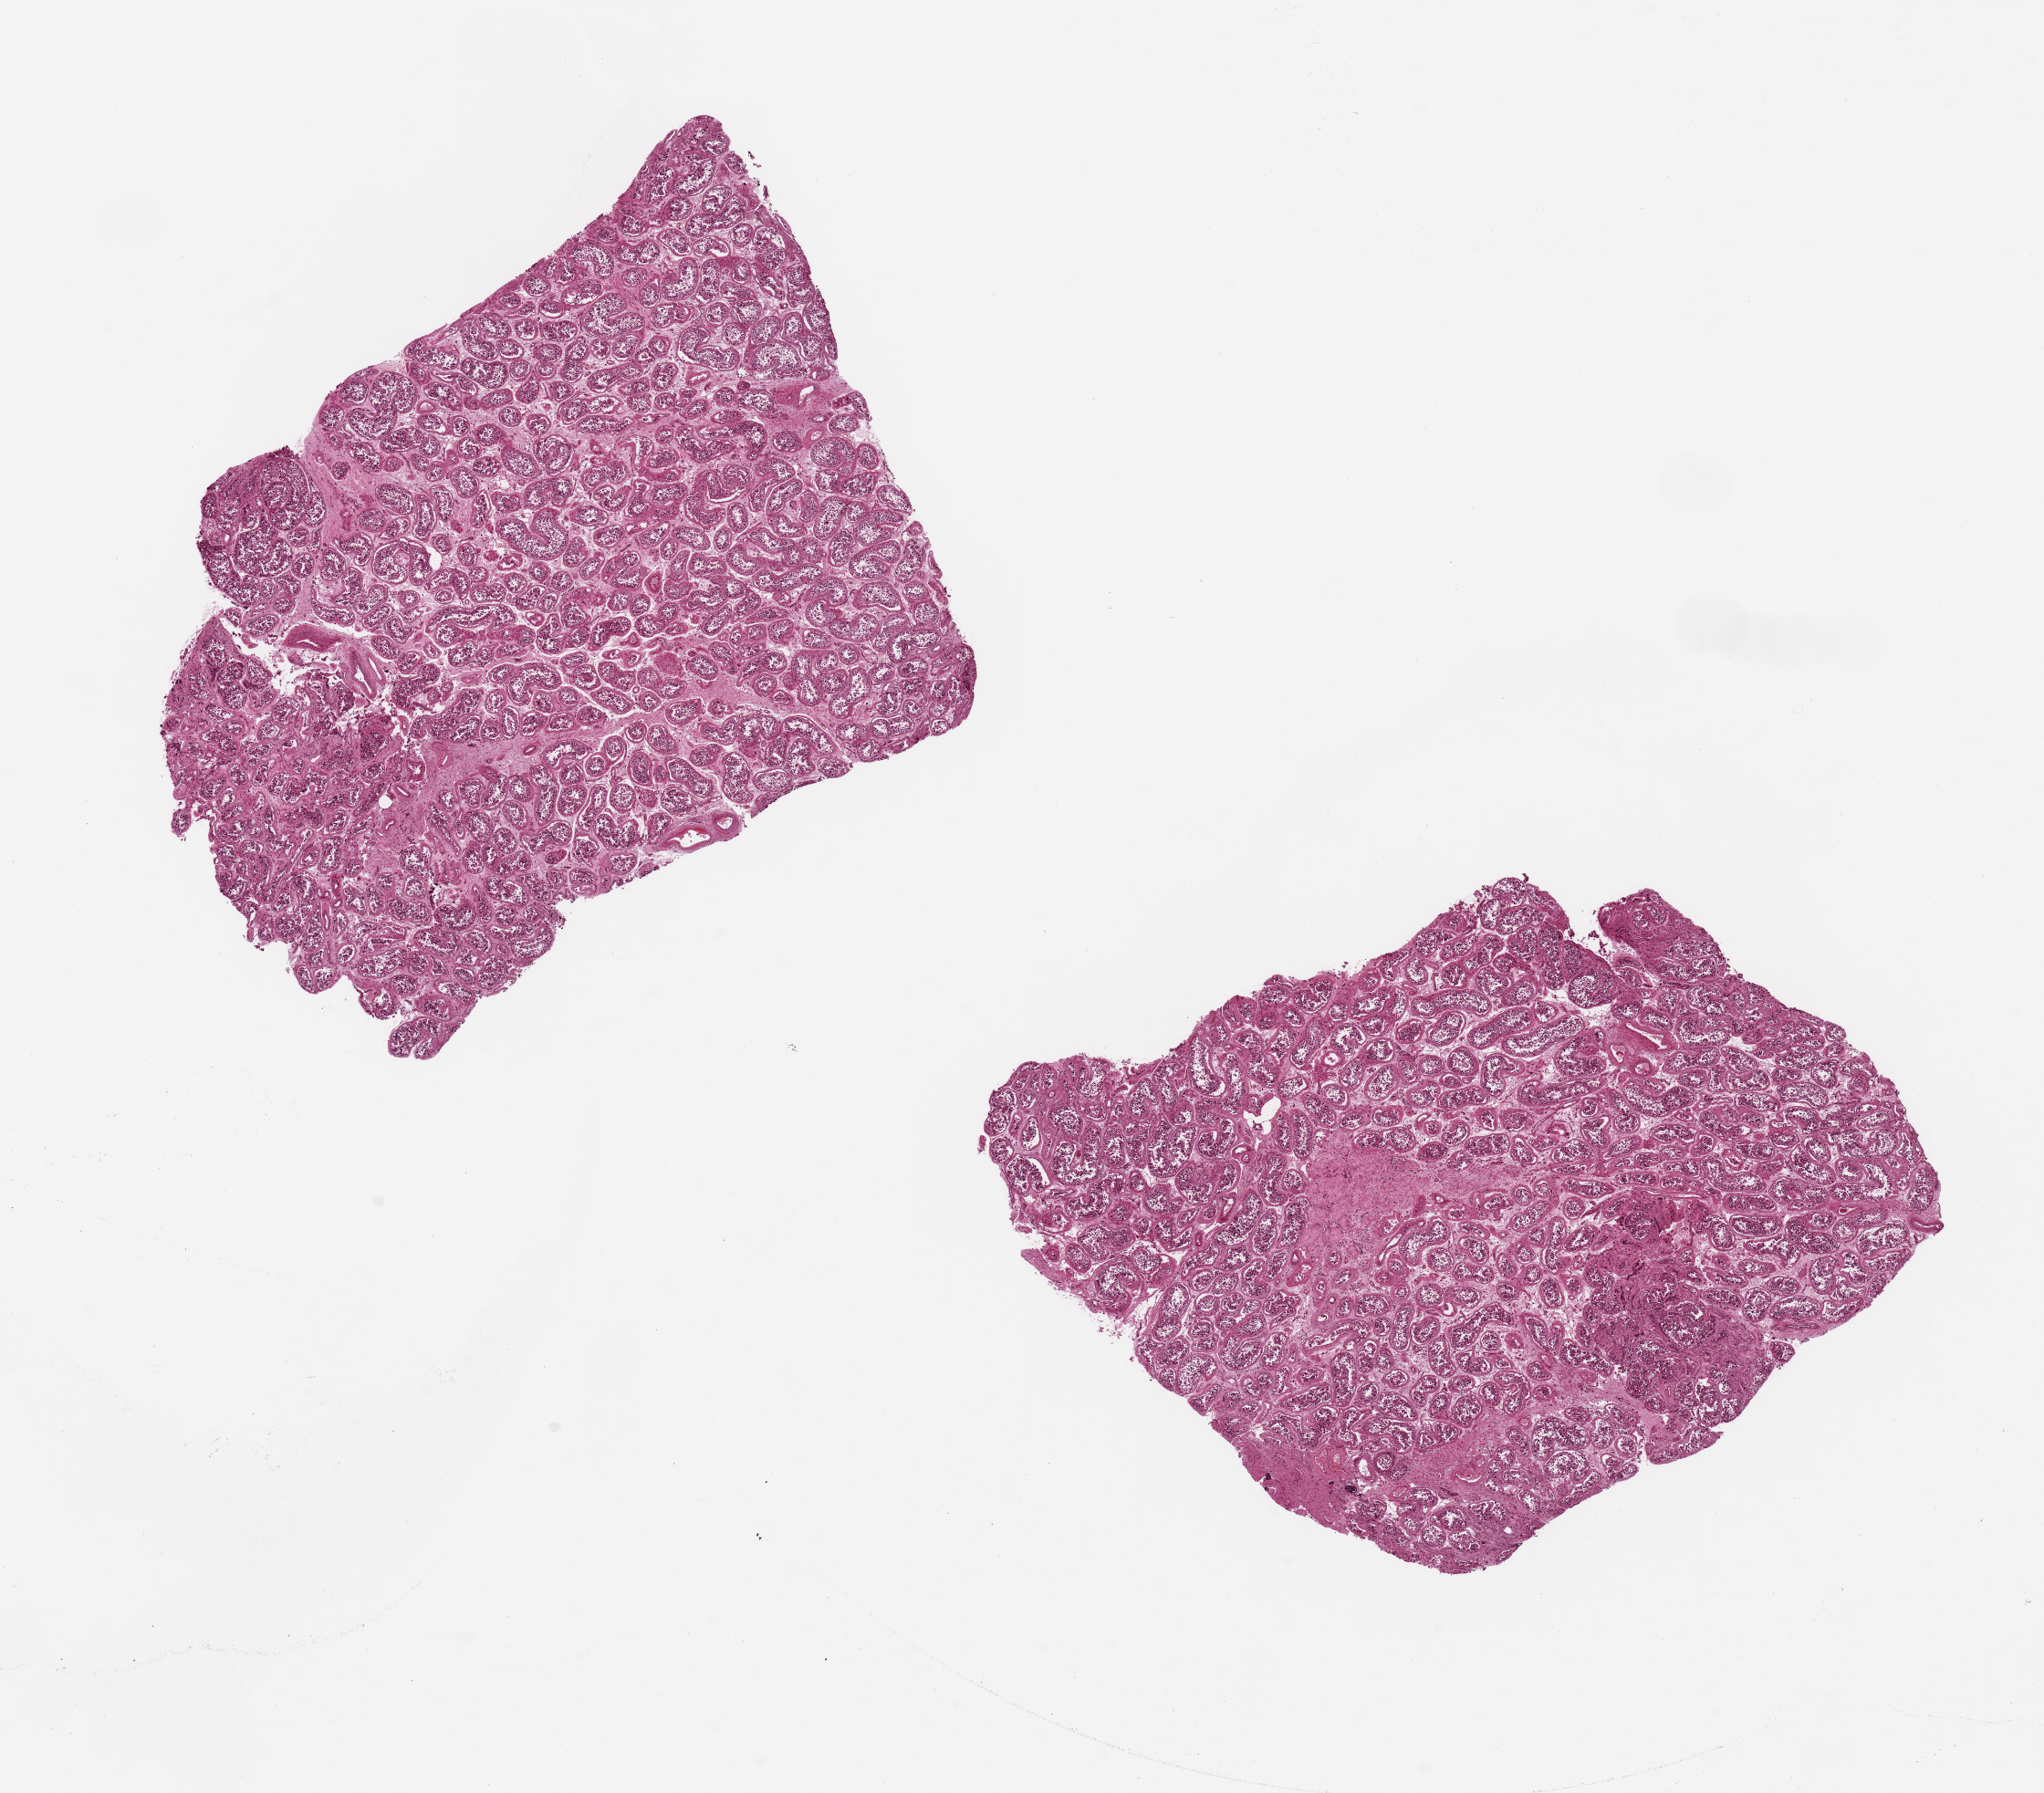
Whole-slide image, H&E stain — whole scanned area (about 17.7 x 15.5 mm, from a 20x scan) shown as a low-resolution overview; PAXgene-fixed, paraffin-embedded tissue; target tissue: testis; tissue donor sample. Donor: male.
Pathologist's review note for this sample: 2 pieces, 7x6 & 6x6mm; spermatogenesis; focal tubular and interstitial fibrosis.